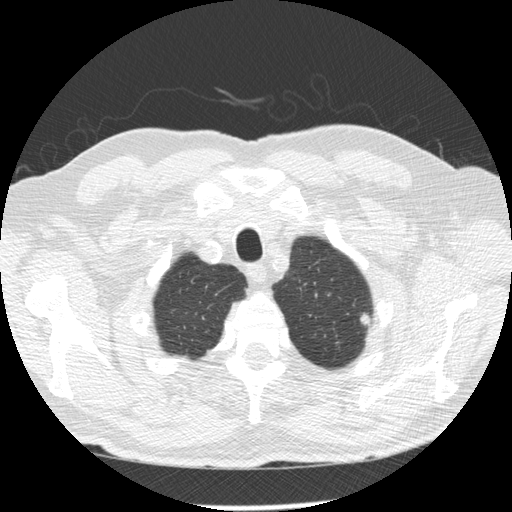
Low-dose screening chest CT, one axial slice; position 235 of 258 along the scan axis; 120 kVp; lung window (W 1500 / L -600 HU); 512 × 512 image matrix, field of view 360 × 360 mm.
Outlined on this slice (expert manual segmentation):
- lesion 1 (tumor, upper lobe of left lung): bounding box <360,314,371,325> (left, top, right, bottom; pixels)